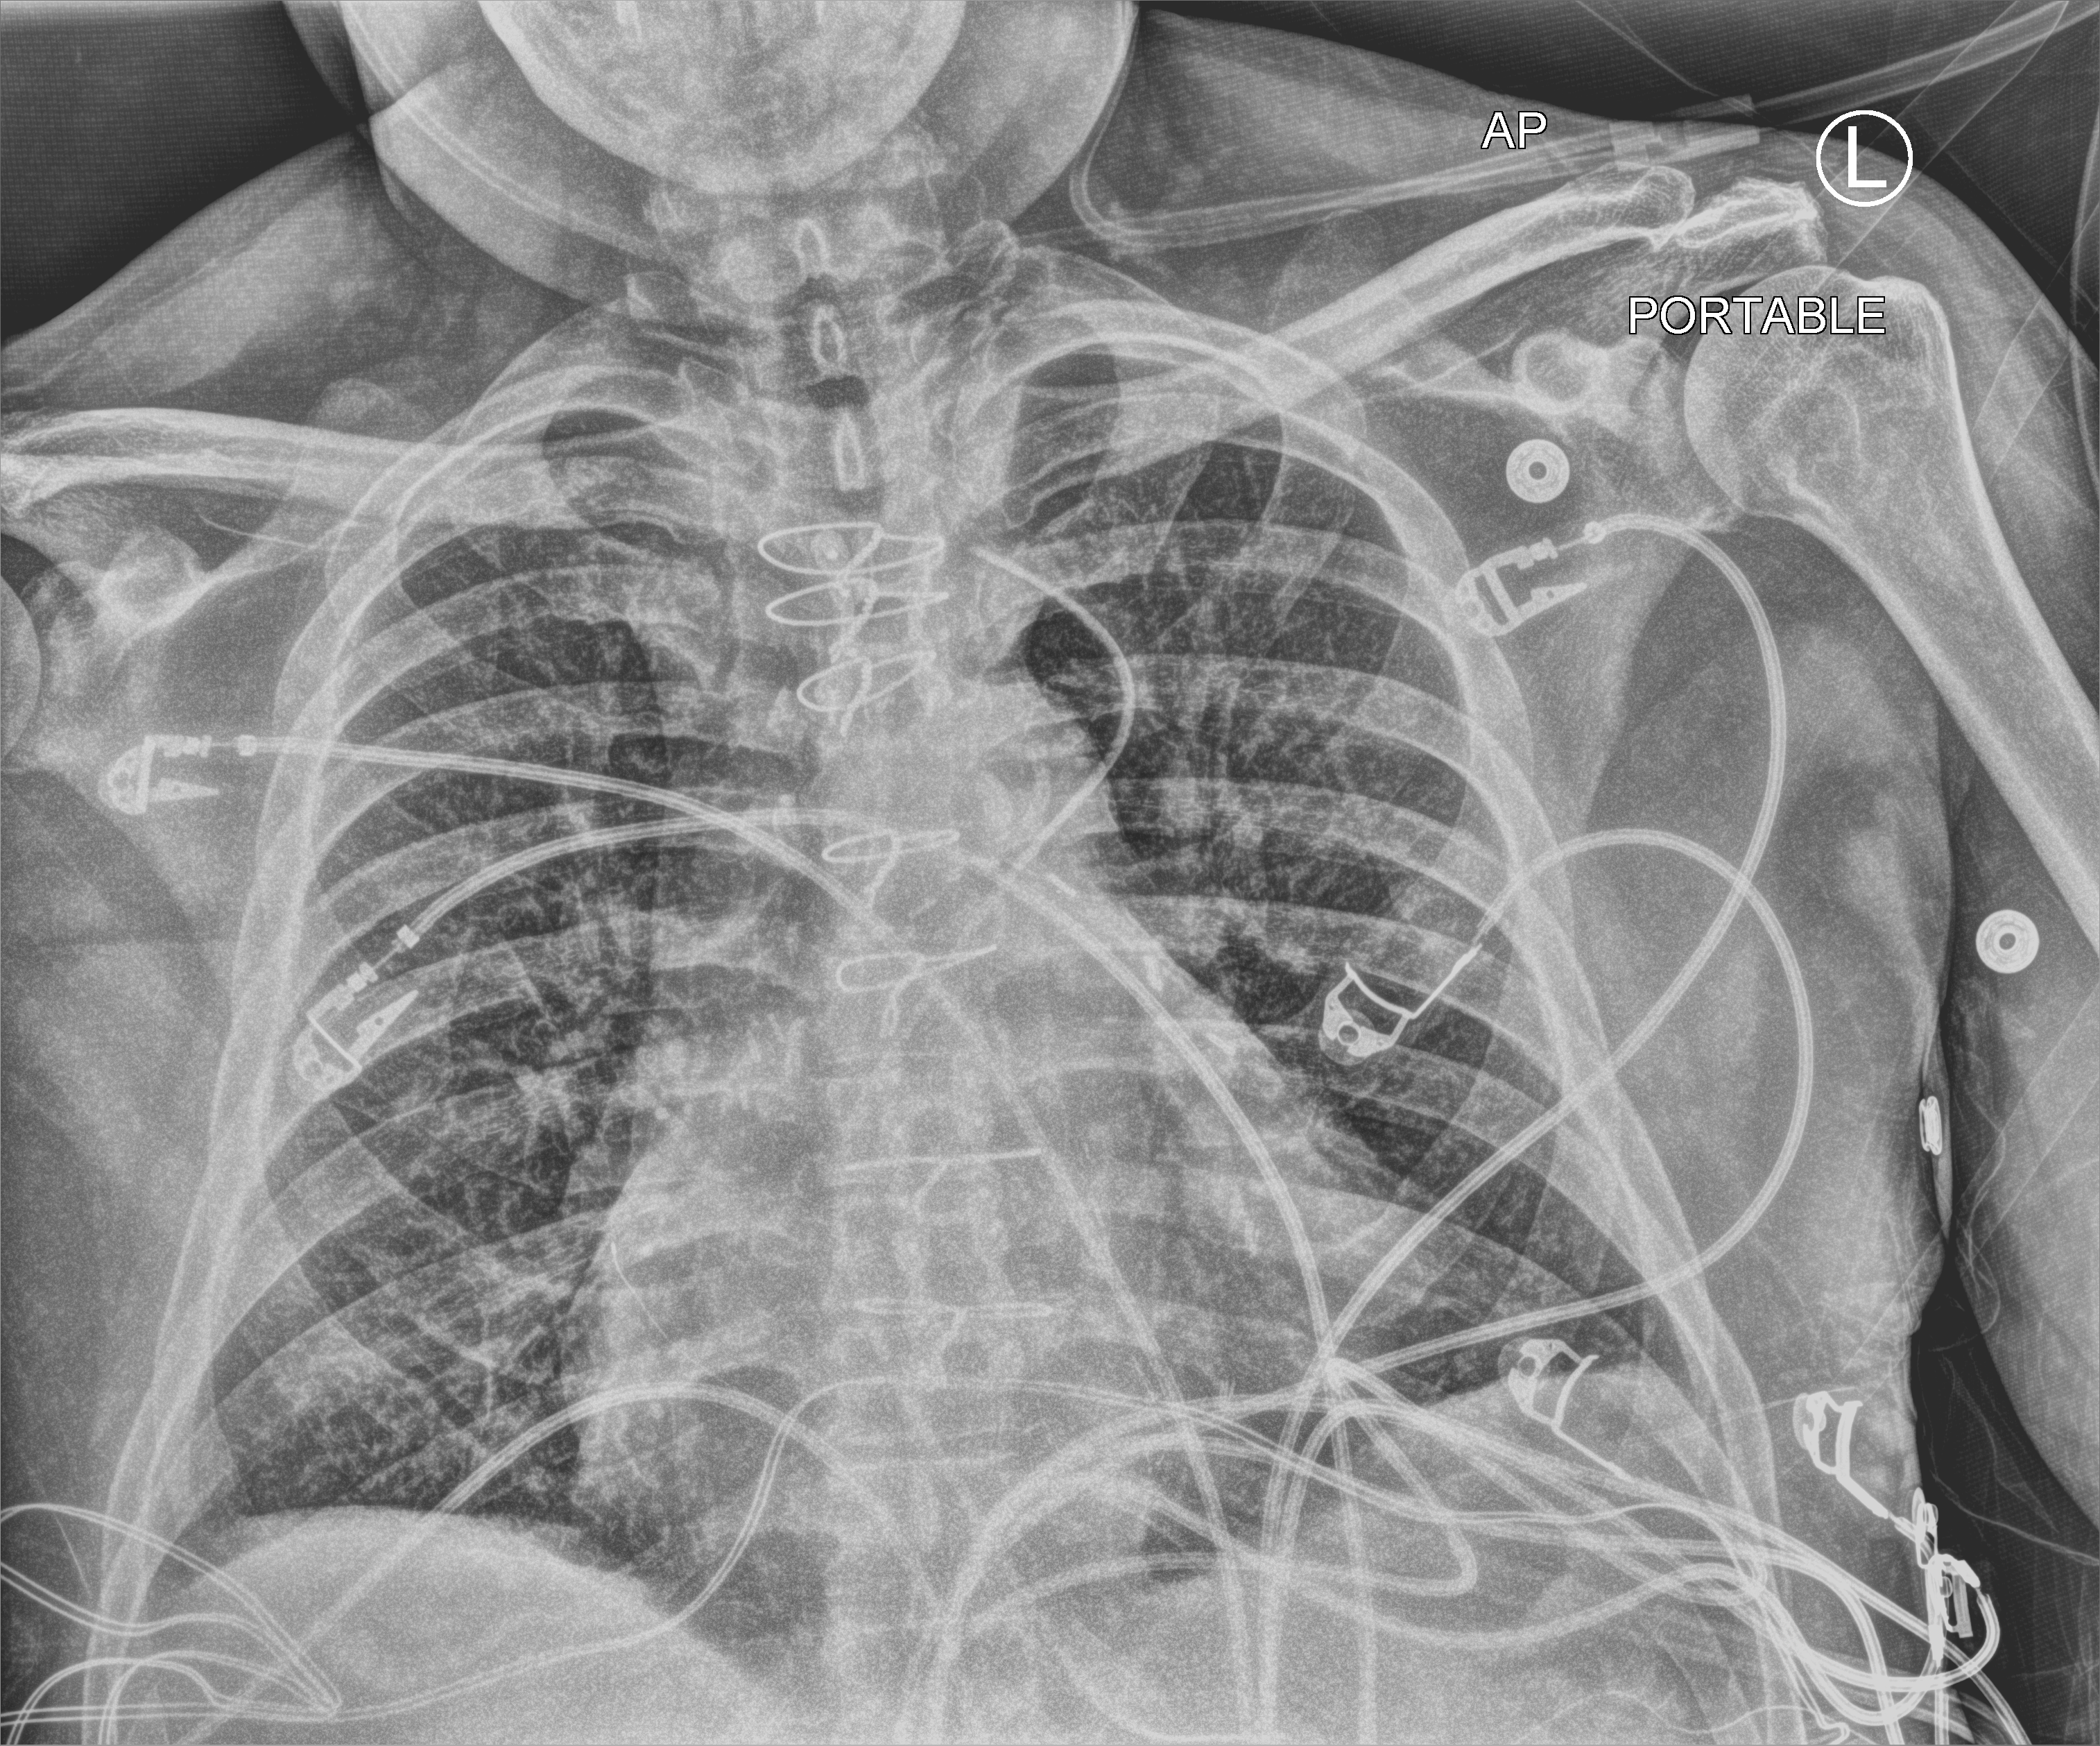
Bedside chest radiograph (computed radiography), anteroposterior (AP) projection. Male patient hospitalised with COVID-19, age 60–74 years.
Hospital-stay facts (about this admission, not read from this image; timing relative to this image not recorded):
- mechanically ventilated during this hospital stay: no
- admitted to intensive care during this hospital stay: no